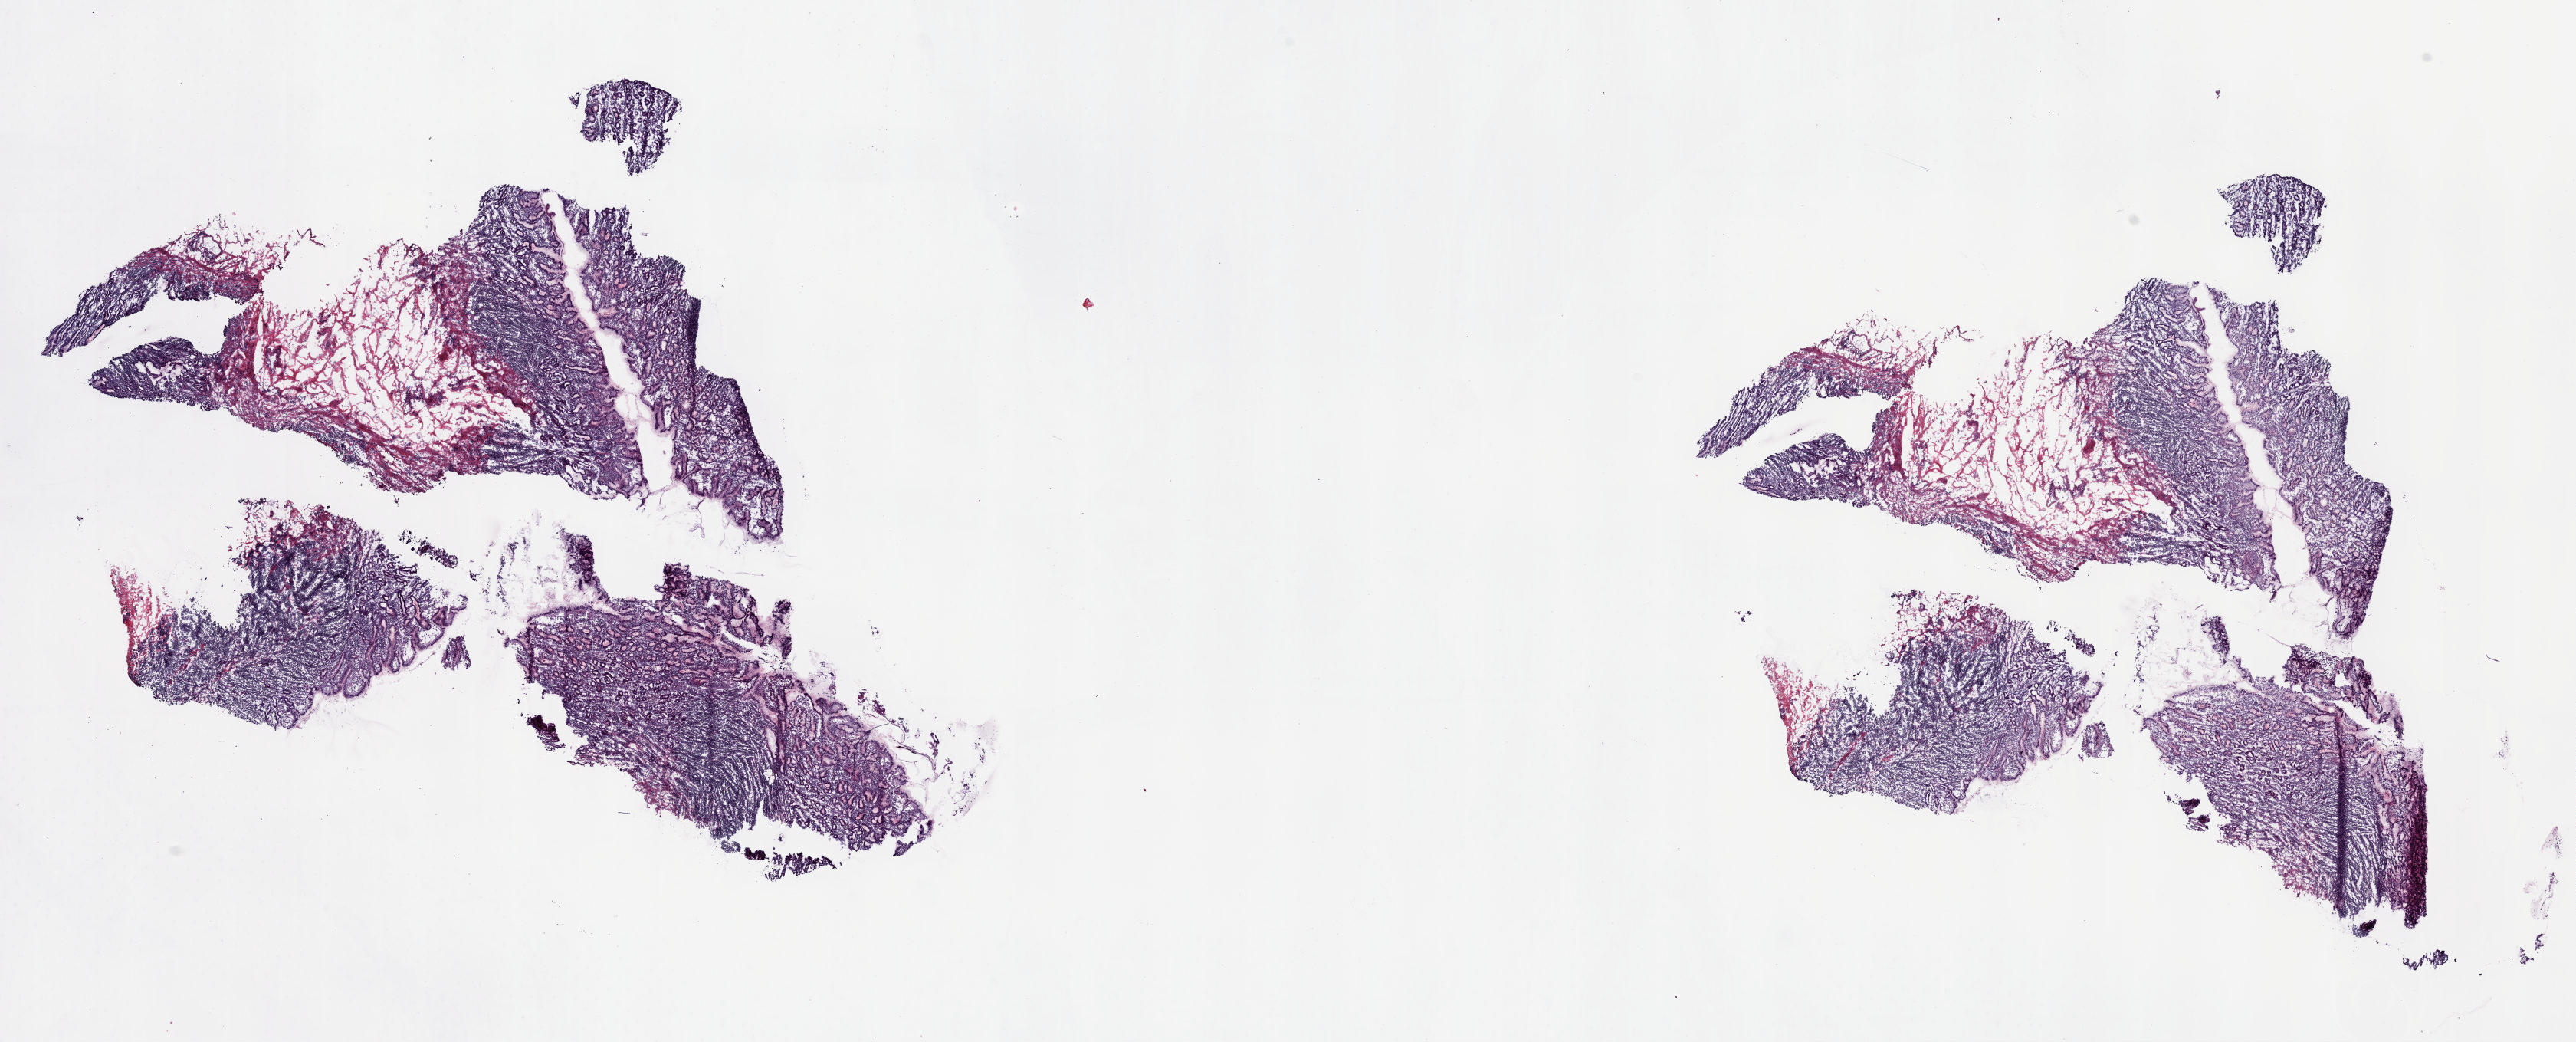
Digitized Hematoxylin and eosin (H&E) stained tissue section (whole slide), whole scanned area (about 26.5 x 10.7 mm, from a 20x scan) shown as a low-resolution overview, frozen section, stomach, solid tissue normal (non-tumour tissue) sample. Male, age 55 years at initial diagnosis. Composition of this section per pathologist review: tumour cells 0%, tumour nuclei 0%, normal cells 100%, stromal cells 0%, necrosis 0%. Infiltration values recorded for this section: lymphocyte infiltration 25%, monocyte infiltration 0%, neutrophil infiltration 0%.
This section: solid tissue normal sample (biorepository sample class). Patient diagnosis: Adenocarcinoma, NOS.